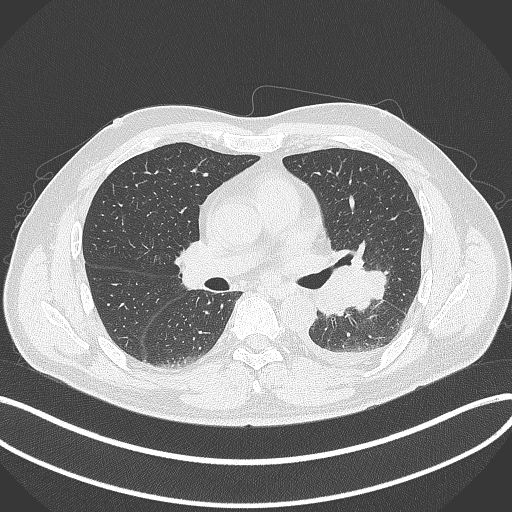
Chest CT, one axial slice. Position 199 of 342 along the scan axis. Reconstruction kernel B70f. Lung window (W 1500 / L -600 HU). 1 mm slice thickness. 512 × 512 image matrix, field of view 400 × 400 mm. Male patient, age 58 years. Case-level facts recorded for this patient, not image findings: clinical TNM (as recorded): T3 N1 M1b; histopathological grade: G3.
Structures marked on this image (bounding box drawn by a radiologist):
- lung tumour (recorded histology: small cell carcinoma): bounding box <320,262,391,316> (left, top, right, bottom; pixels)